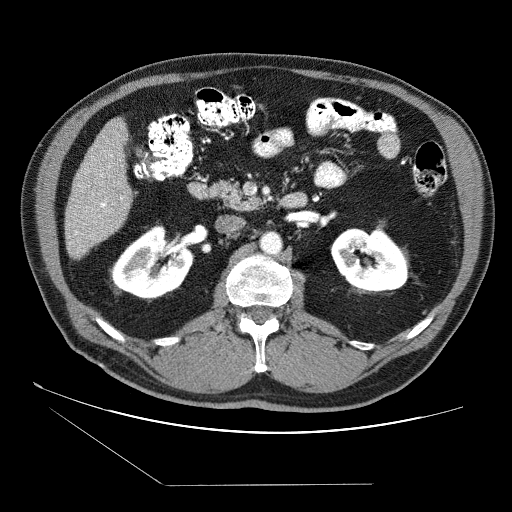
Contrast-enhanced abdominal CT (liver protocol), one axial slice; slice 18 of 87 in the series (ordered by position); reconstruction kernel STANDARD; soft-tissue window (W 400 / L 40 HU); 2.5 mm slice thickness; 512 × 512 image matrix, field of view 400 × 400 mm. From the clinical record (not read from this slice): diagnosis: hepatocellular carcinoma (patient treated with transarterial chemoembolisation; whether this scan precedes or follows treatment is not stated here); TNM stage (as recorded): Stage-II; Child-Pugh class: B; tumour nodularity: multinodular; tumour size: 2.6 cm.
Structures marked on this image (semi-automatic segmentation, software-assisted and operator-edited):
- liver parenchyma outside the tumour (the mass and vessels are separate outlines, so this box may not span the whole liver): box from (x=64, y=118) to (x=132, y=258) px
- liver vessels: (x=70, y=154)–(x=123, y=244)